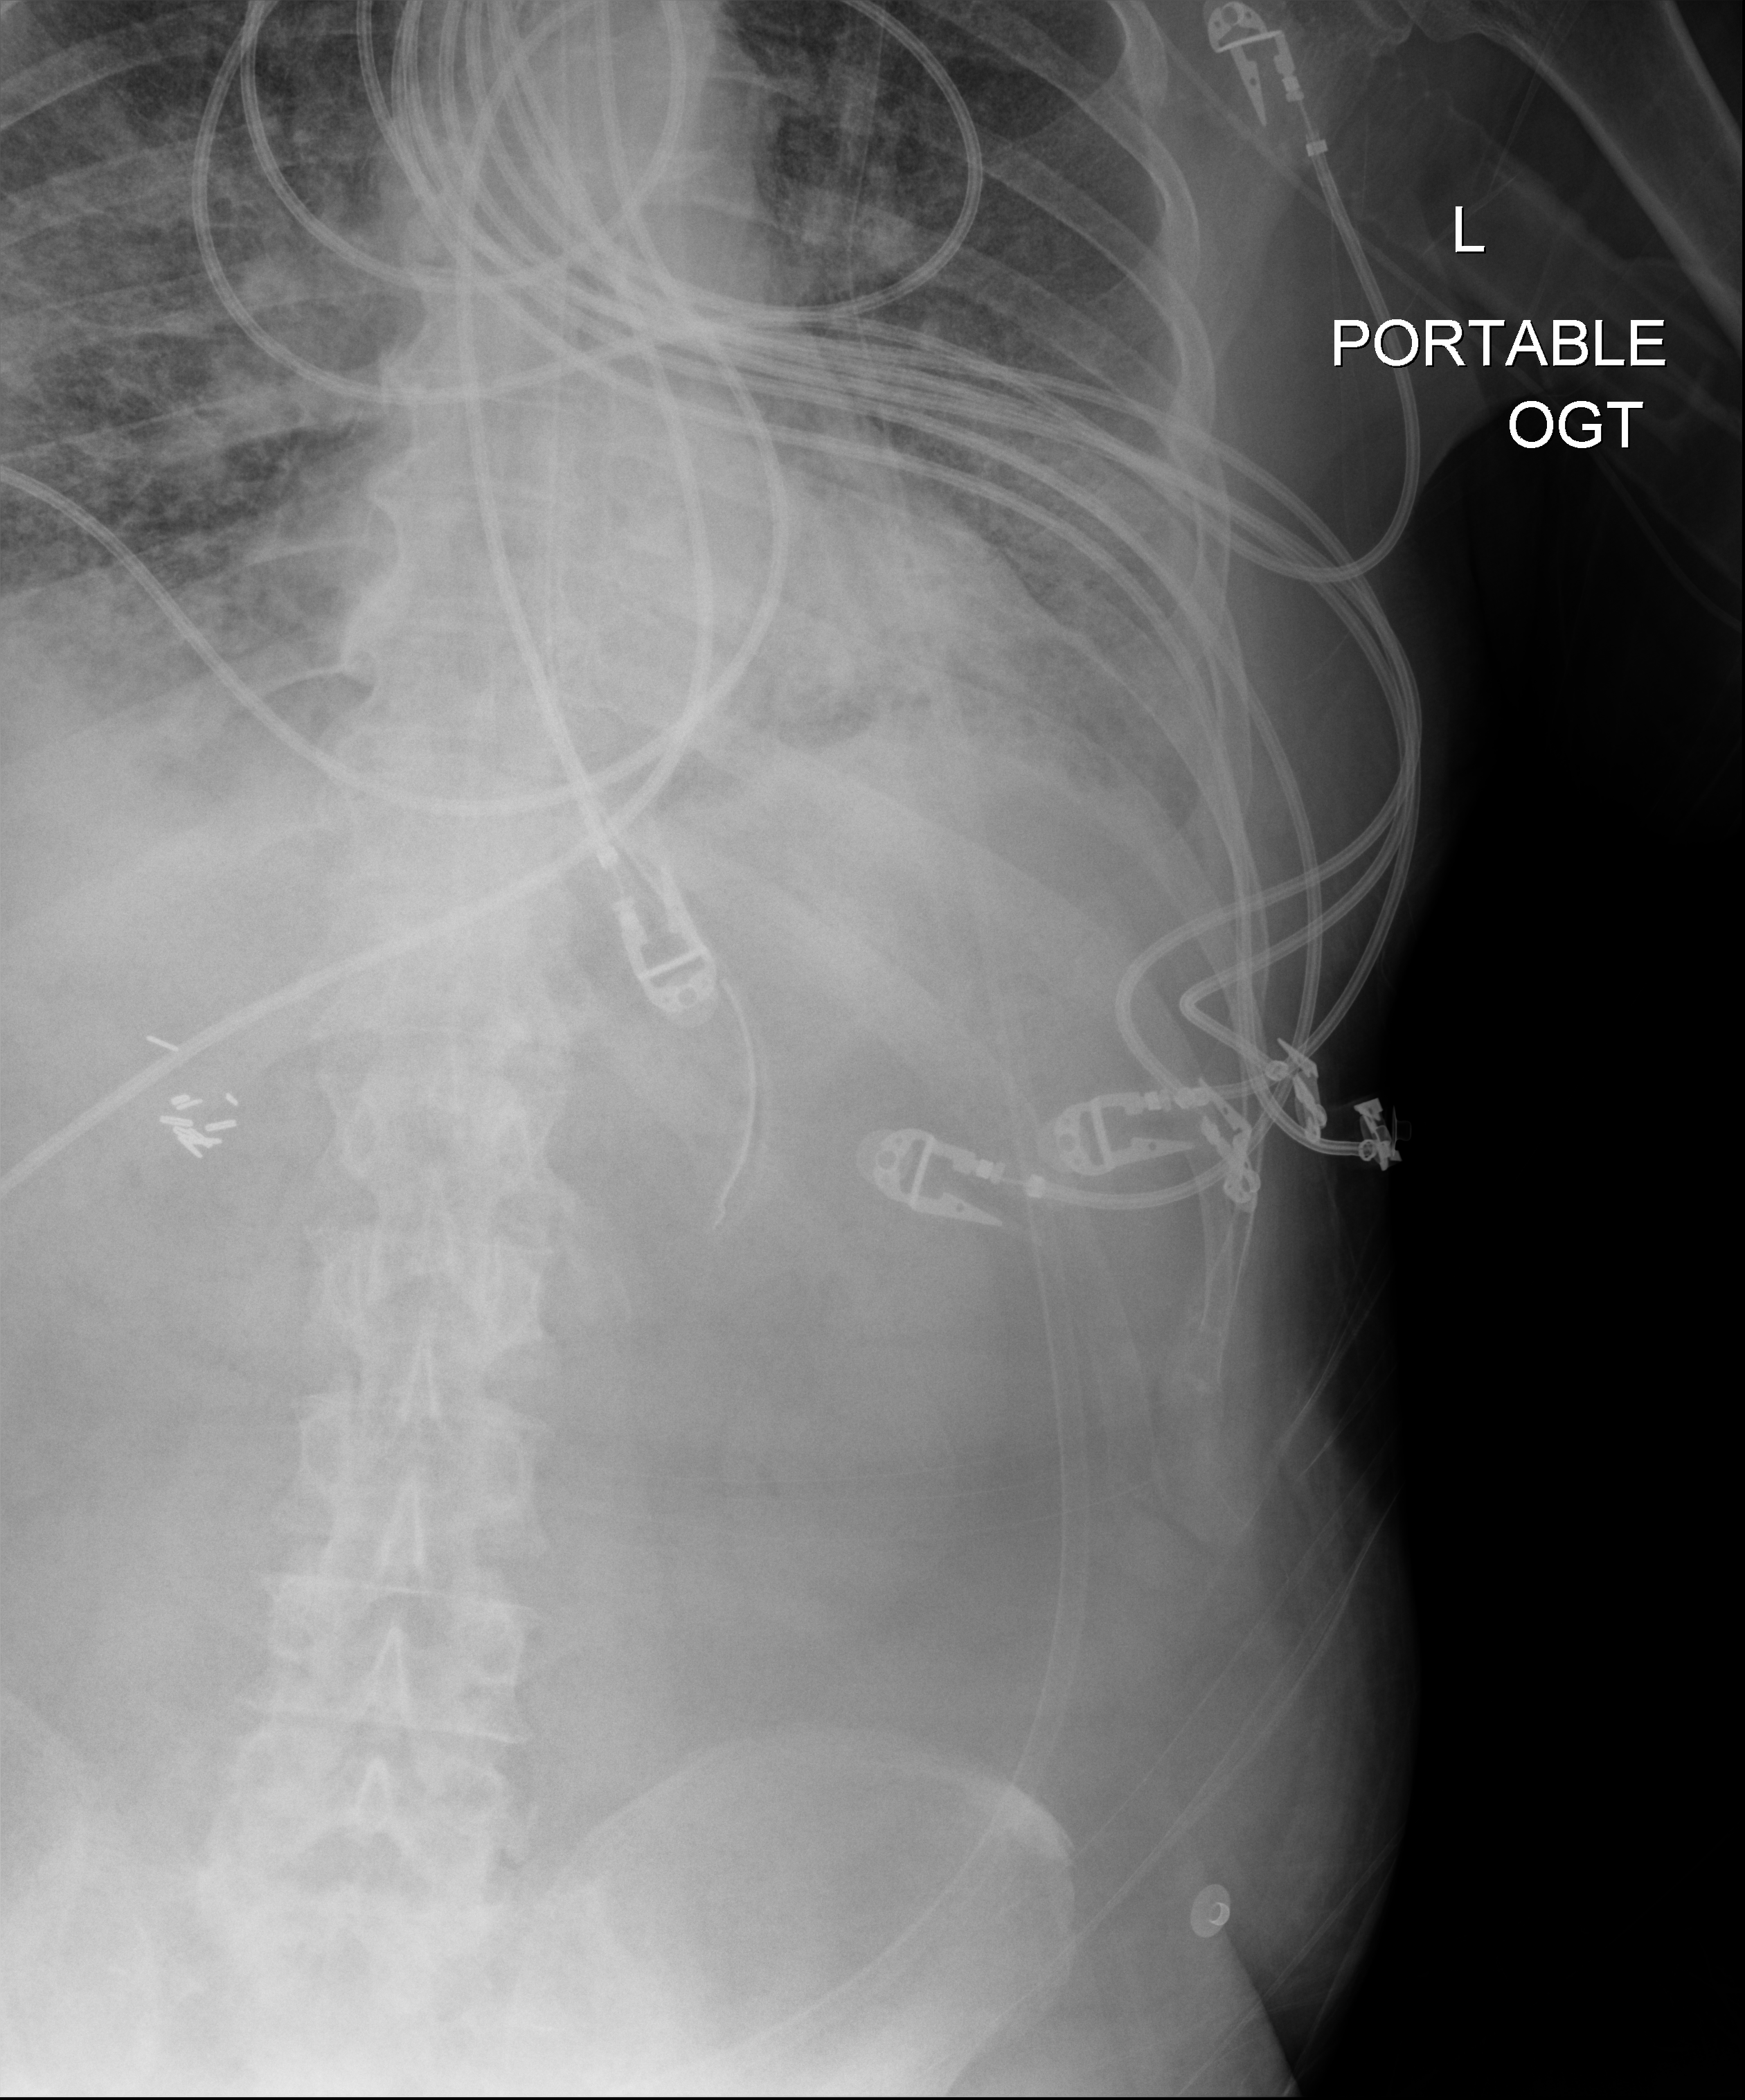
Chest X-ray. Male patient hospitalised with COVID-19, age 75–90 years.
Admission-level facts for this patient (not findings on this image; timing relative to this image not recorded):
- COPD (admission record): no
- admitted to intensive care during this hospital stay: yes